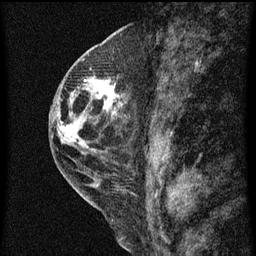
Breast MRI (dynamic contrast-enhanced), one sagittal slice. Position 26 of 60 along the scan axis. Dynamic contrast-enhanced series, image 2 of 3 at this slice position (ordered by acquisition). 1.5 T. TE 4.2 ms, TR 8 ms. 2 mm slice thickness. 256 × 256 image matrix, field of view 180 × 180 mm. Patient: female, 48 years.
Outlined on this slice (semi-automatically segmented with operator editing):
- analysis volume of interest (the breast-tissue region the enhancement analysis was run in; not a lesion): bounding box [x1, y1, x2, y2] px = [89, 72, 123, 113]
- tumour enhancement mask (voxels above the 70 % enhancement threshold inside the analysis volume of interest): [94, 80, 119, 113]